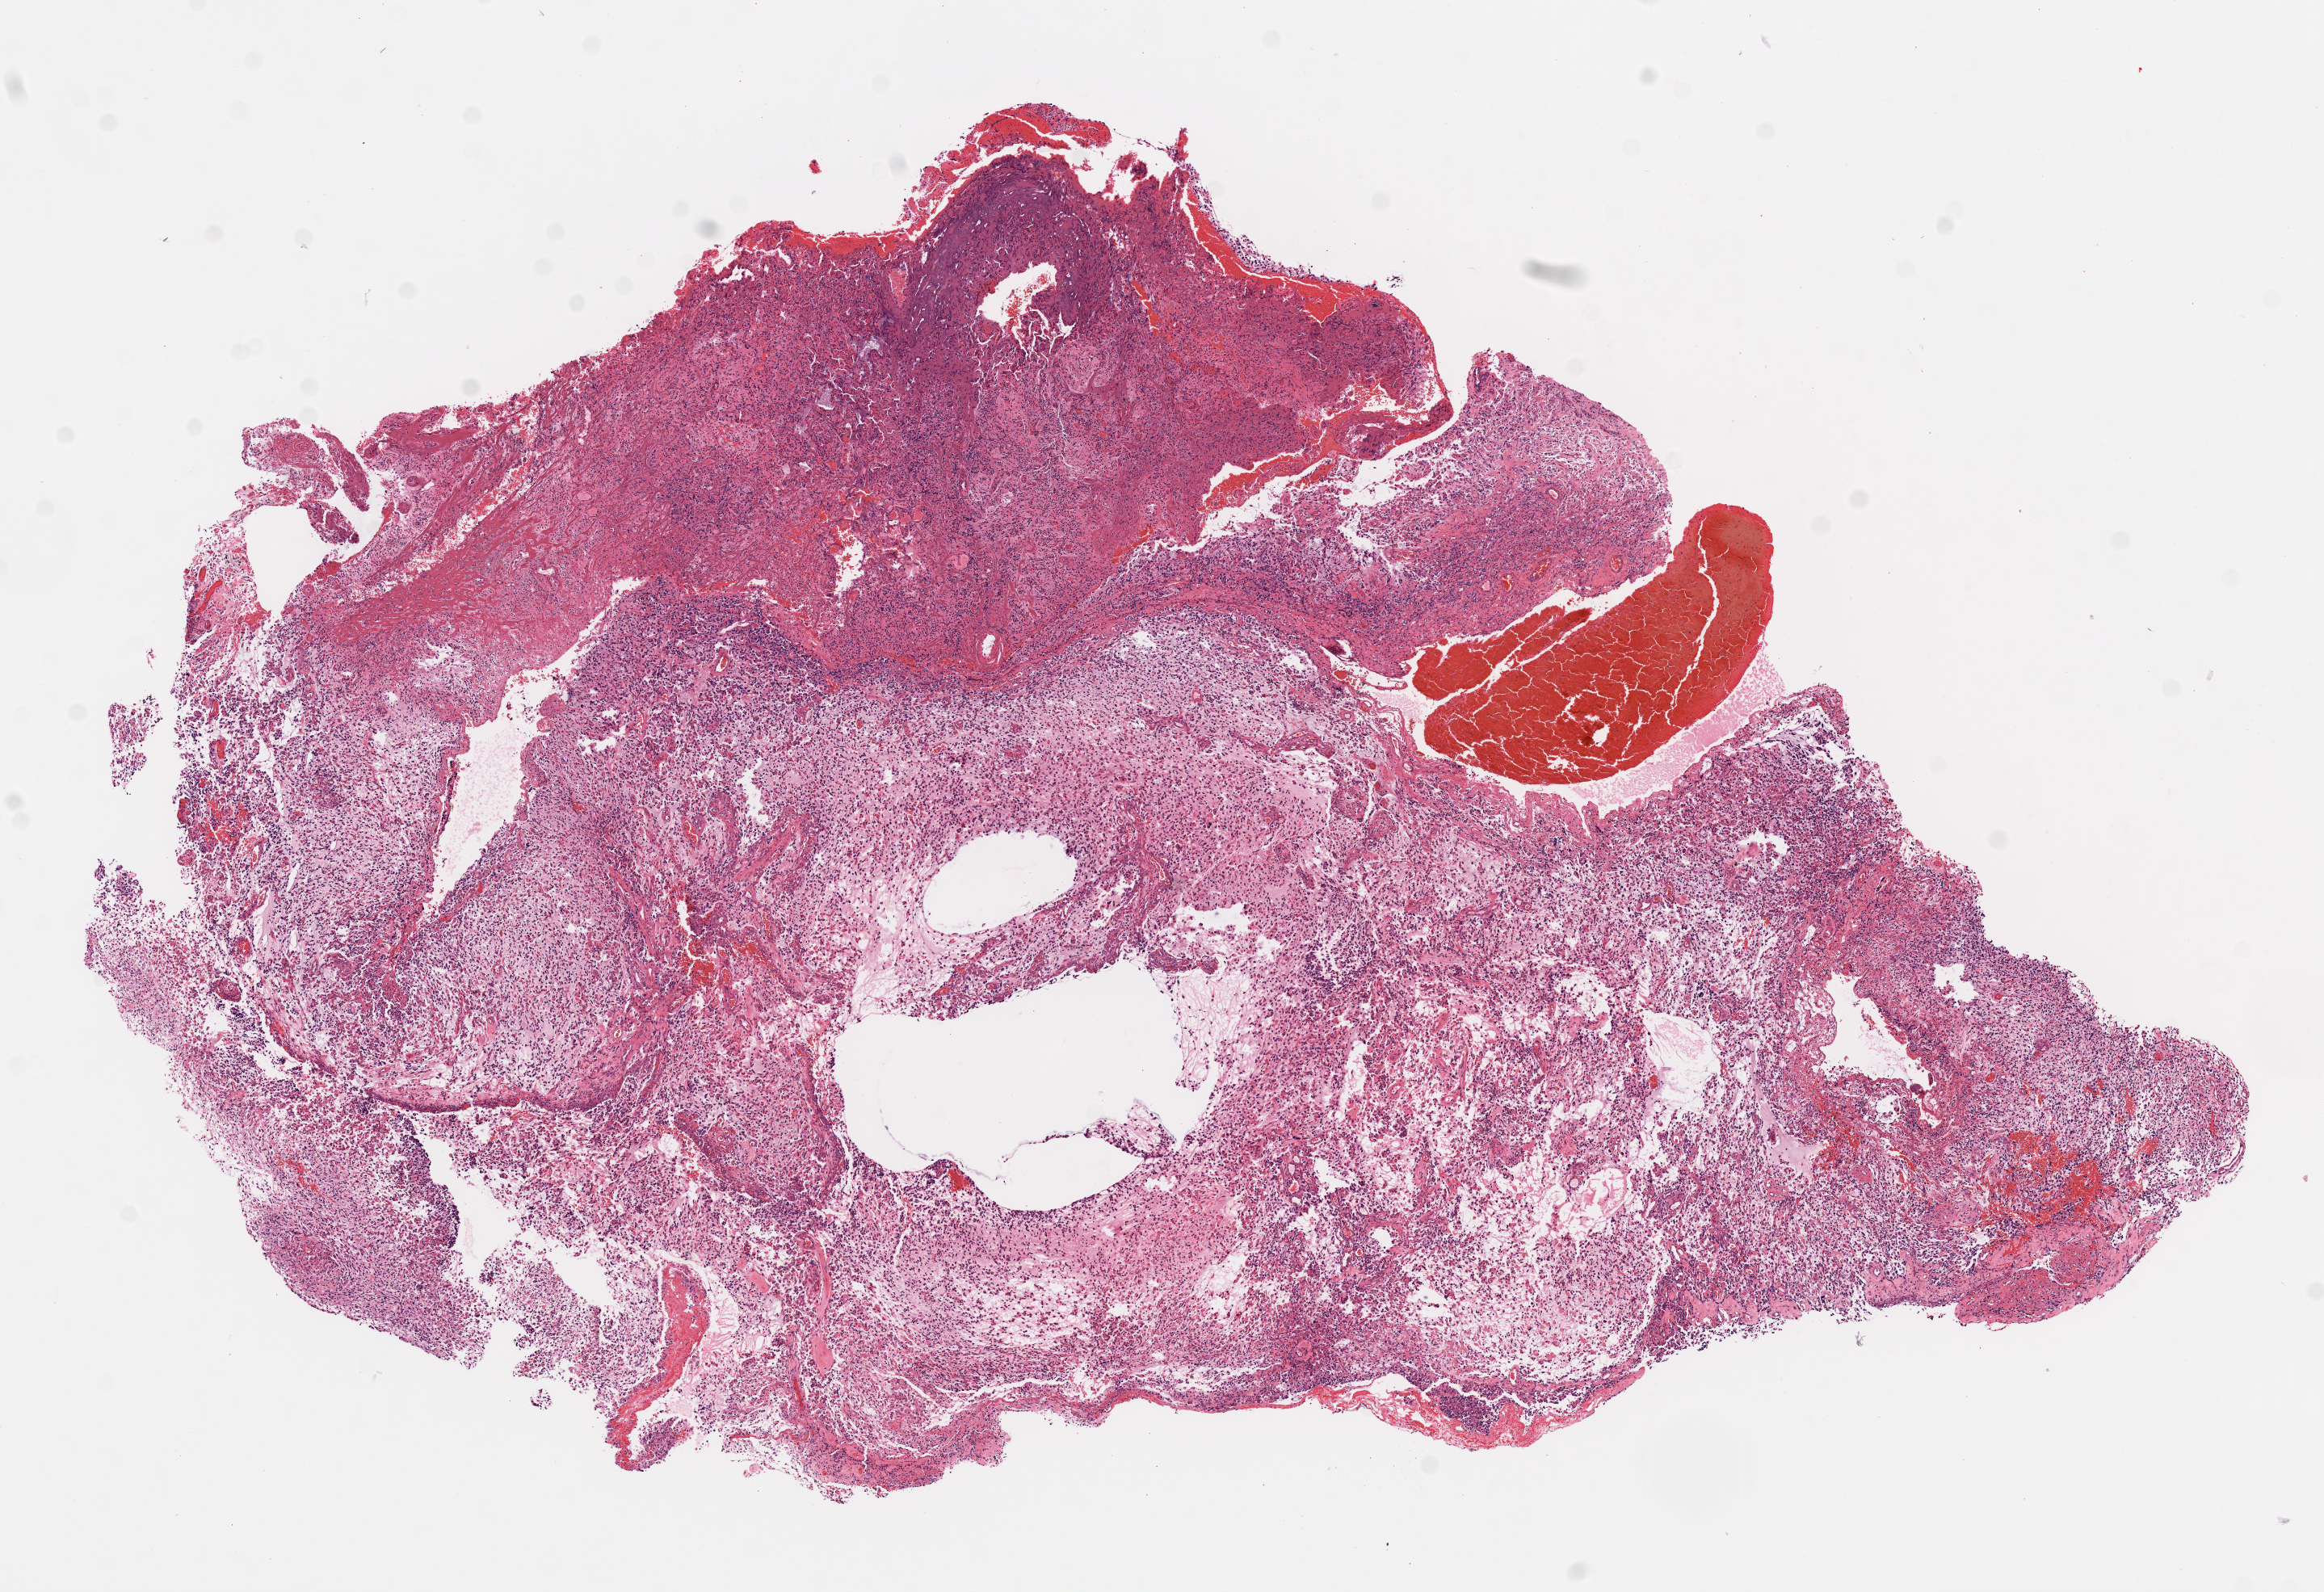
Digitized Hematoxylin and eosin (H&E) stained tissue section (whole slide) — shown as a low-resolution overview of the whole scanned area (about 11.6 x 7.9 mm, slide scanned at 20x). Formalin-fixed paraffin-embedded (FFPE) diagnostic section. Brain, primary tumour sample. Male, age 66 years at initial diagnosis.
Pathologic diagnosis: Glioblastoma.